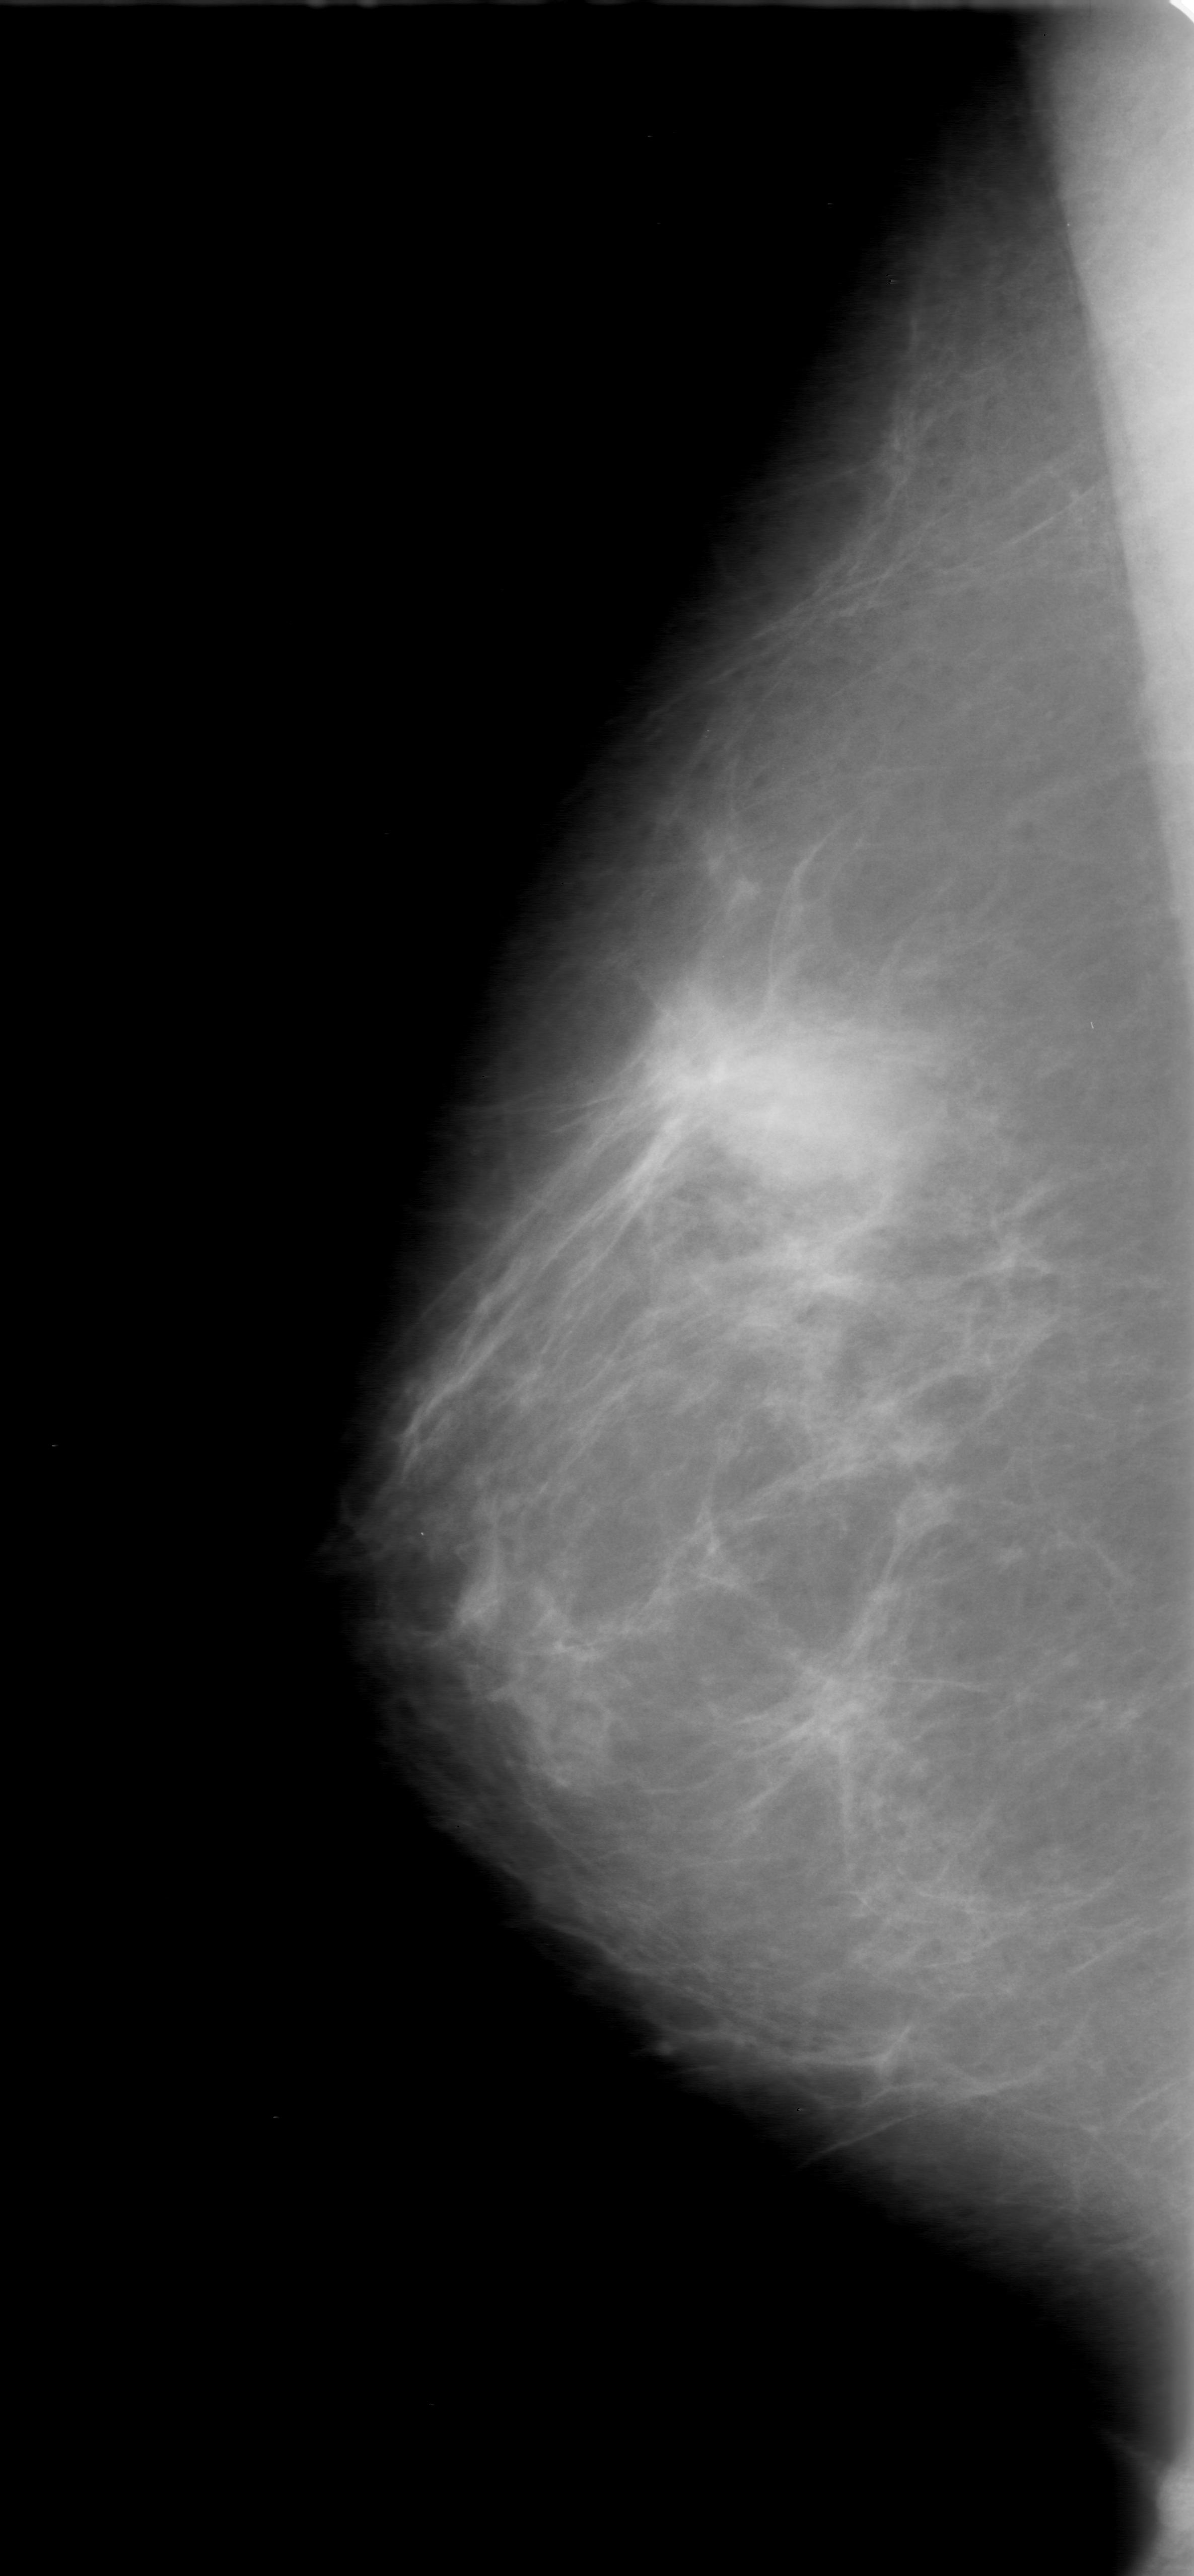
Scanned film-screen mammogram, right breast, mediolateral oblique (MLO) view, breast composition: almost entirely fatty (BI-RADS density category 1 of 4).
Radiologist-marked abnormalities on this image: mass, shape oval, margins obscured; BI-RADS assessment category 0 (incomplete: needs additional imaging); pathology result (as recorded, not read from the image): benign.